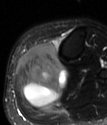
MRI of an extremity soft-tissue mass, one axial slice; position 29 of 78 along the scan axis; T2-weighted fat-saturated; MR volume resampled by the dataset authors to the PET/CT grid (not the native acquisition matrix); 107 × 125 image matrix, field of view 104 × 122 mm. Female patient. Case-level facts recorded for this patient, not image findings: histological type: extraskeletal high grade osteogenic sarcoma; grade: high; site of the primary tumour: left calf.
Outlined on this slice (expert contour drawn on MRI and transferred to this co-registered scan by the dataset authors):
- gross tumour volume (mass): bounding box [x1, y1, x2, y2] px = [16, 43, 67, 108]